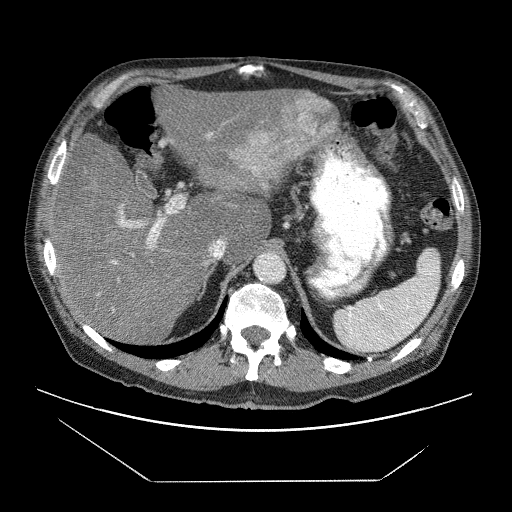
Contrast-enhanced abdominal CT (liver protocol), one axial slice; position 44 of 83 along the scan axis; reconstruction kernel STANDARD; 120 kVp; soft-tissue window (W 400 / L 40 HU); 2.5 mm slice thickness; 512 × 512 image matrix, field of view 420 × 420 mm. Case-level facts recorded for this patient, not image findings: diagnosis: hepatocellular carcinoma (patient treated with transarterial chemoembolisation; whether this scan precedes or follows treatment is not stated here); TNM stage (as recorded): Stage-IVB; Child-Pugh class: B; tumour nodularity: uninodular.
Annotated regions visible in this slice (semi-automatically segmented with operator editing):
- liver parenchyma outside the tumour (the mass and vessels are separate outlines, so this box may not span the whole liver): bounding box <50,82,336,340> (left, top, right, bottom; pixels)
- mass: <234,90,337,179>
- liver vessels: <57,133,212,312>